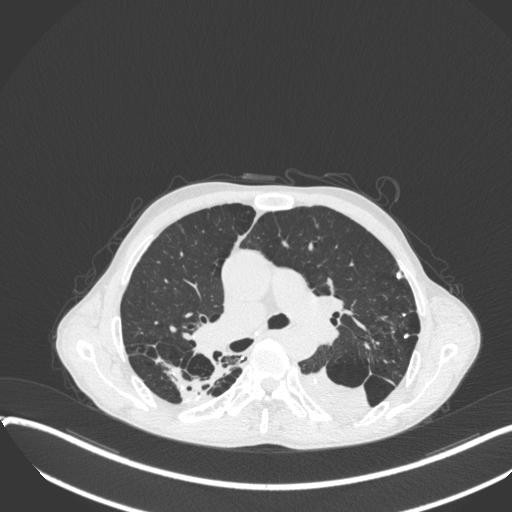
Chest CT, one axial slice. Position 238 of 400 along the scan axis. Reconstruction kernel B31f. Lung window (W 1500 / L -600 HU). 512 × 512 image matrix, field of view 400 × 400 mm. Patient: male, 57 years. From the clinical record (not read from this slice): clinical TNM (as recorded): T4 N0 M0.
Annotated regions visible in this slice (rectangle marked by the reading radiologist):
- lung tumour (recorded histology: squamous cell carcinoma): bounding box <300,364,373,417> (left, top, right, bottom; pixels)